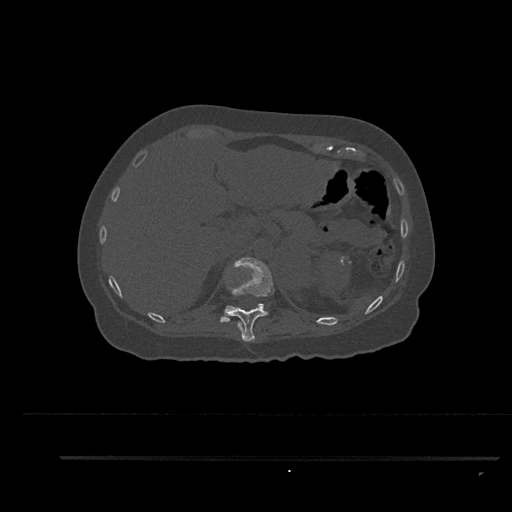
CT including the spine, one axial slice. Position 300 of 797 along the scan axis. Reconstruction kernel Br40s/3. 120 kVp. Bone window (W 1800 / L 400 HU). 0.5 mm slice thickness. 512 × 512 image matrix, field of view 408 × 408 mm. Patient: female, 44 years. Case-level facts recorded for this patient, not image findings: primary cancer: renal; vertebrae with lytic lesions (as recorded): L1.
Structures marked on this image (semi-automatic segmentation, software-assisted and operator-edited):
- T11 vertebra: bounding box [x1, y1, x2, y2] px = [226, 257, 275, 342]
- T12 vertebra: [219, 303, 265, 323]